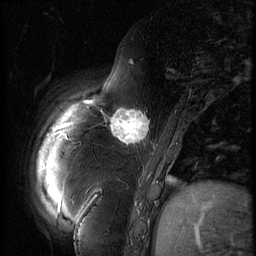
Breast MRI (dynamic contrast-enhanced), one sagittal slice. 3 images stored at this slice position (order not interpretable as contrast timing). 1.5 T. TE 4.2 ms, TR 9 ms. 2.5 mm slice thickness. 256 × 256 image matrix, field of view 180 × 180 mm. Female patient, age 57 years. Case-level facts recorded for this patient, not image findings: setting: breast cancer imaged before/during neoadjuvant chemotherapy; receptor status: triple-negative.
Annotated regions visible in this slice (semi-automatic segmentation, software-assisted and operator-edited):
- analysis volume of interest (the breast-tissue region the enhancement analysis was run in; not a lesion): bounding box [x1, y1, x2, y2] px = [106, 101, 157, 152]
- tumour enhancement mask (voxels above the 140 % enhancement threshold inside the analysis volume of interest): [111, 109, 150, 145]